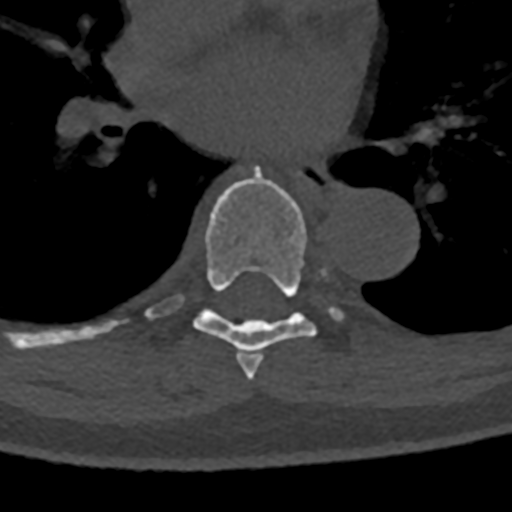
CT including the spine, one axial slice; position 761 of 797 along the scan axis; reconstruction kernel Br40s/3; 120 kVp; bone window (W 1800 / L 400 HU); 0.5 mm slice thickness; 512 × 512 image matrix, field of view 160 × 160 mm. Patient: male, 74 years. From the clinical record (not read from this slice): primary cancer: renal; vertebrae with lytic lesions (as recorded): T10, L1, L2, L3, L4, L5.
Outlined on this slice (semi-automatic segmentation, software-assisted and operator-edited):
- T6 vertebra: bounding box [x1, y1, x2, y2] px = [245, 355, 264, 380]
- T7 vertebra: [70, 168, 344, 371]
- T8 vertebra: [71, 329, 106, 342]